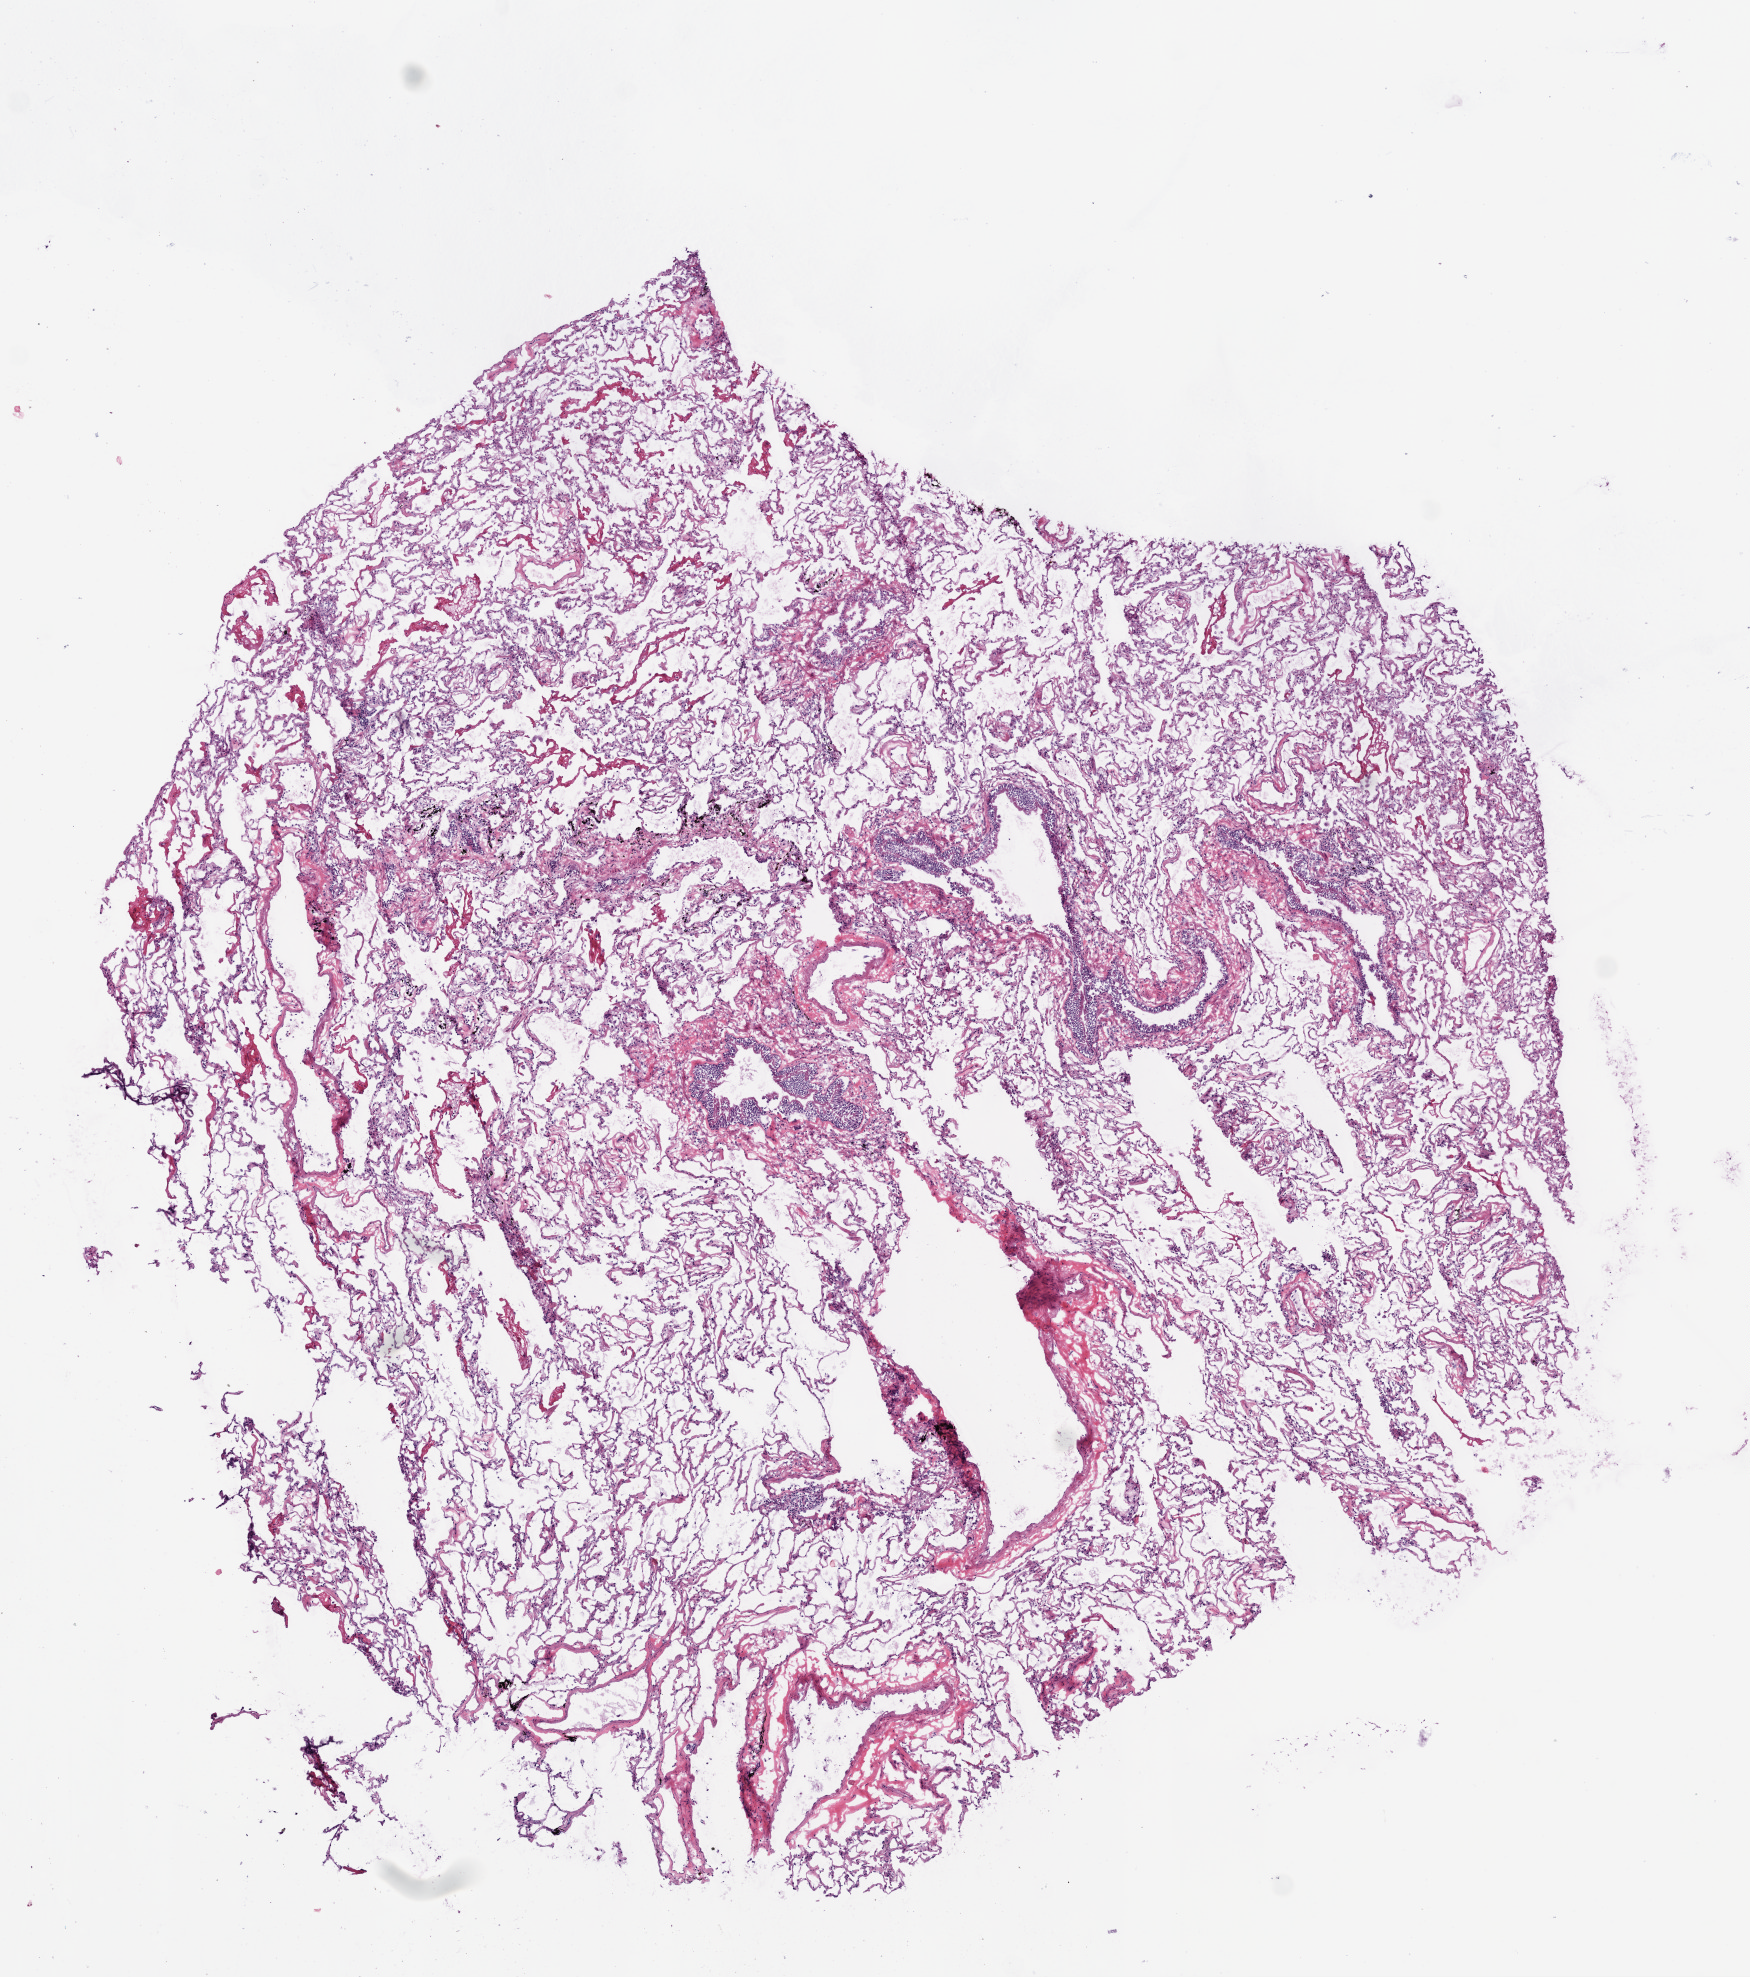
Digitized H&E tissue section (whole slide) — a low-resolution overview of the entire scanned area, about 7.0 x 7.9 mm, frozen section from the bottom of the tissue portion, lung, solid tissue normal (non-tumour tissue) sample. Patient: male, age at initial diagnosis 81 years.
- this section: solid tissue normal (non-tumour) sample from the same patient
- patient diagnosis: Squamous cell carcinoma, NOS (lower lobe, lung)